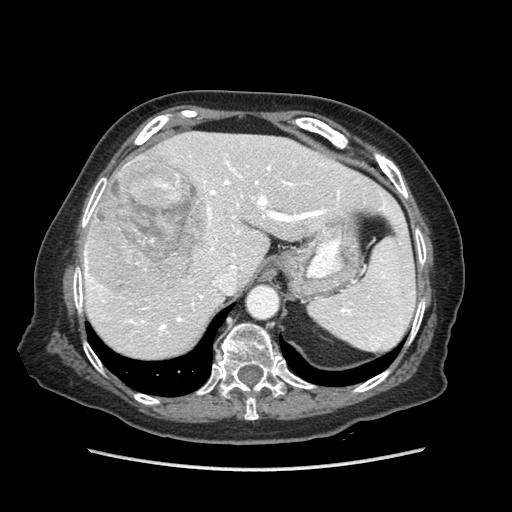
Contrast-enhanced abdominal CT (liver protocol), one axial slice; position 60 of 89 along the scan axis; soft-tissue window (W 400 / L 40 HU); 2.5 mm slice thickness; 512 × 512 image matrix, field of view 360 × 360 mm. Case-level facts recorded for this patient, not image findings: diagnosis: hepatocellular carcinoma (patient treated with transarterial chemoembolisation; whether this scan precedes or follows treatment is not stated here); TNM stage (as recorded): Stage-IIIA; Child-Pugh class: A; tumour nodularity: multinodular; tumour size: 11 cm.
Structures marked on this image (semi-automatic segmentation, software-assisted and operator-edited):
- liver parenchyma outside the tumour (the mass and vessels are separate outlines, so this box may not span the whole liver): bounding box <82,132,403,358> (left, top, right, bottom; pixels)
- mass: <85,160,207,295>
- liver vessels: <85,160,386,334>